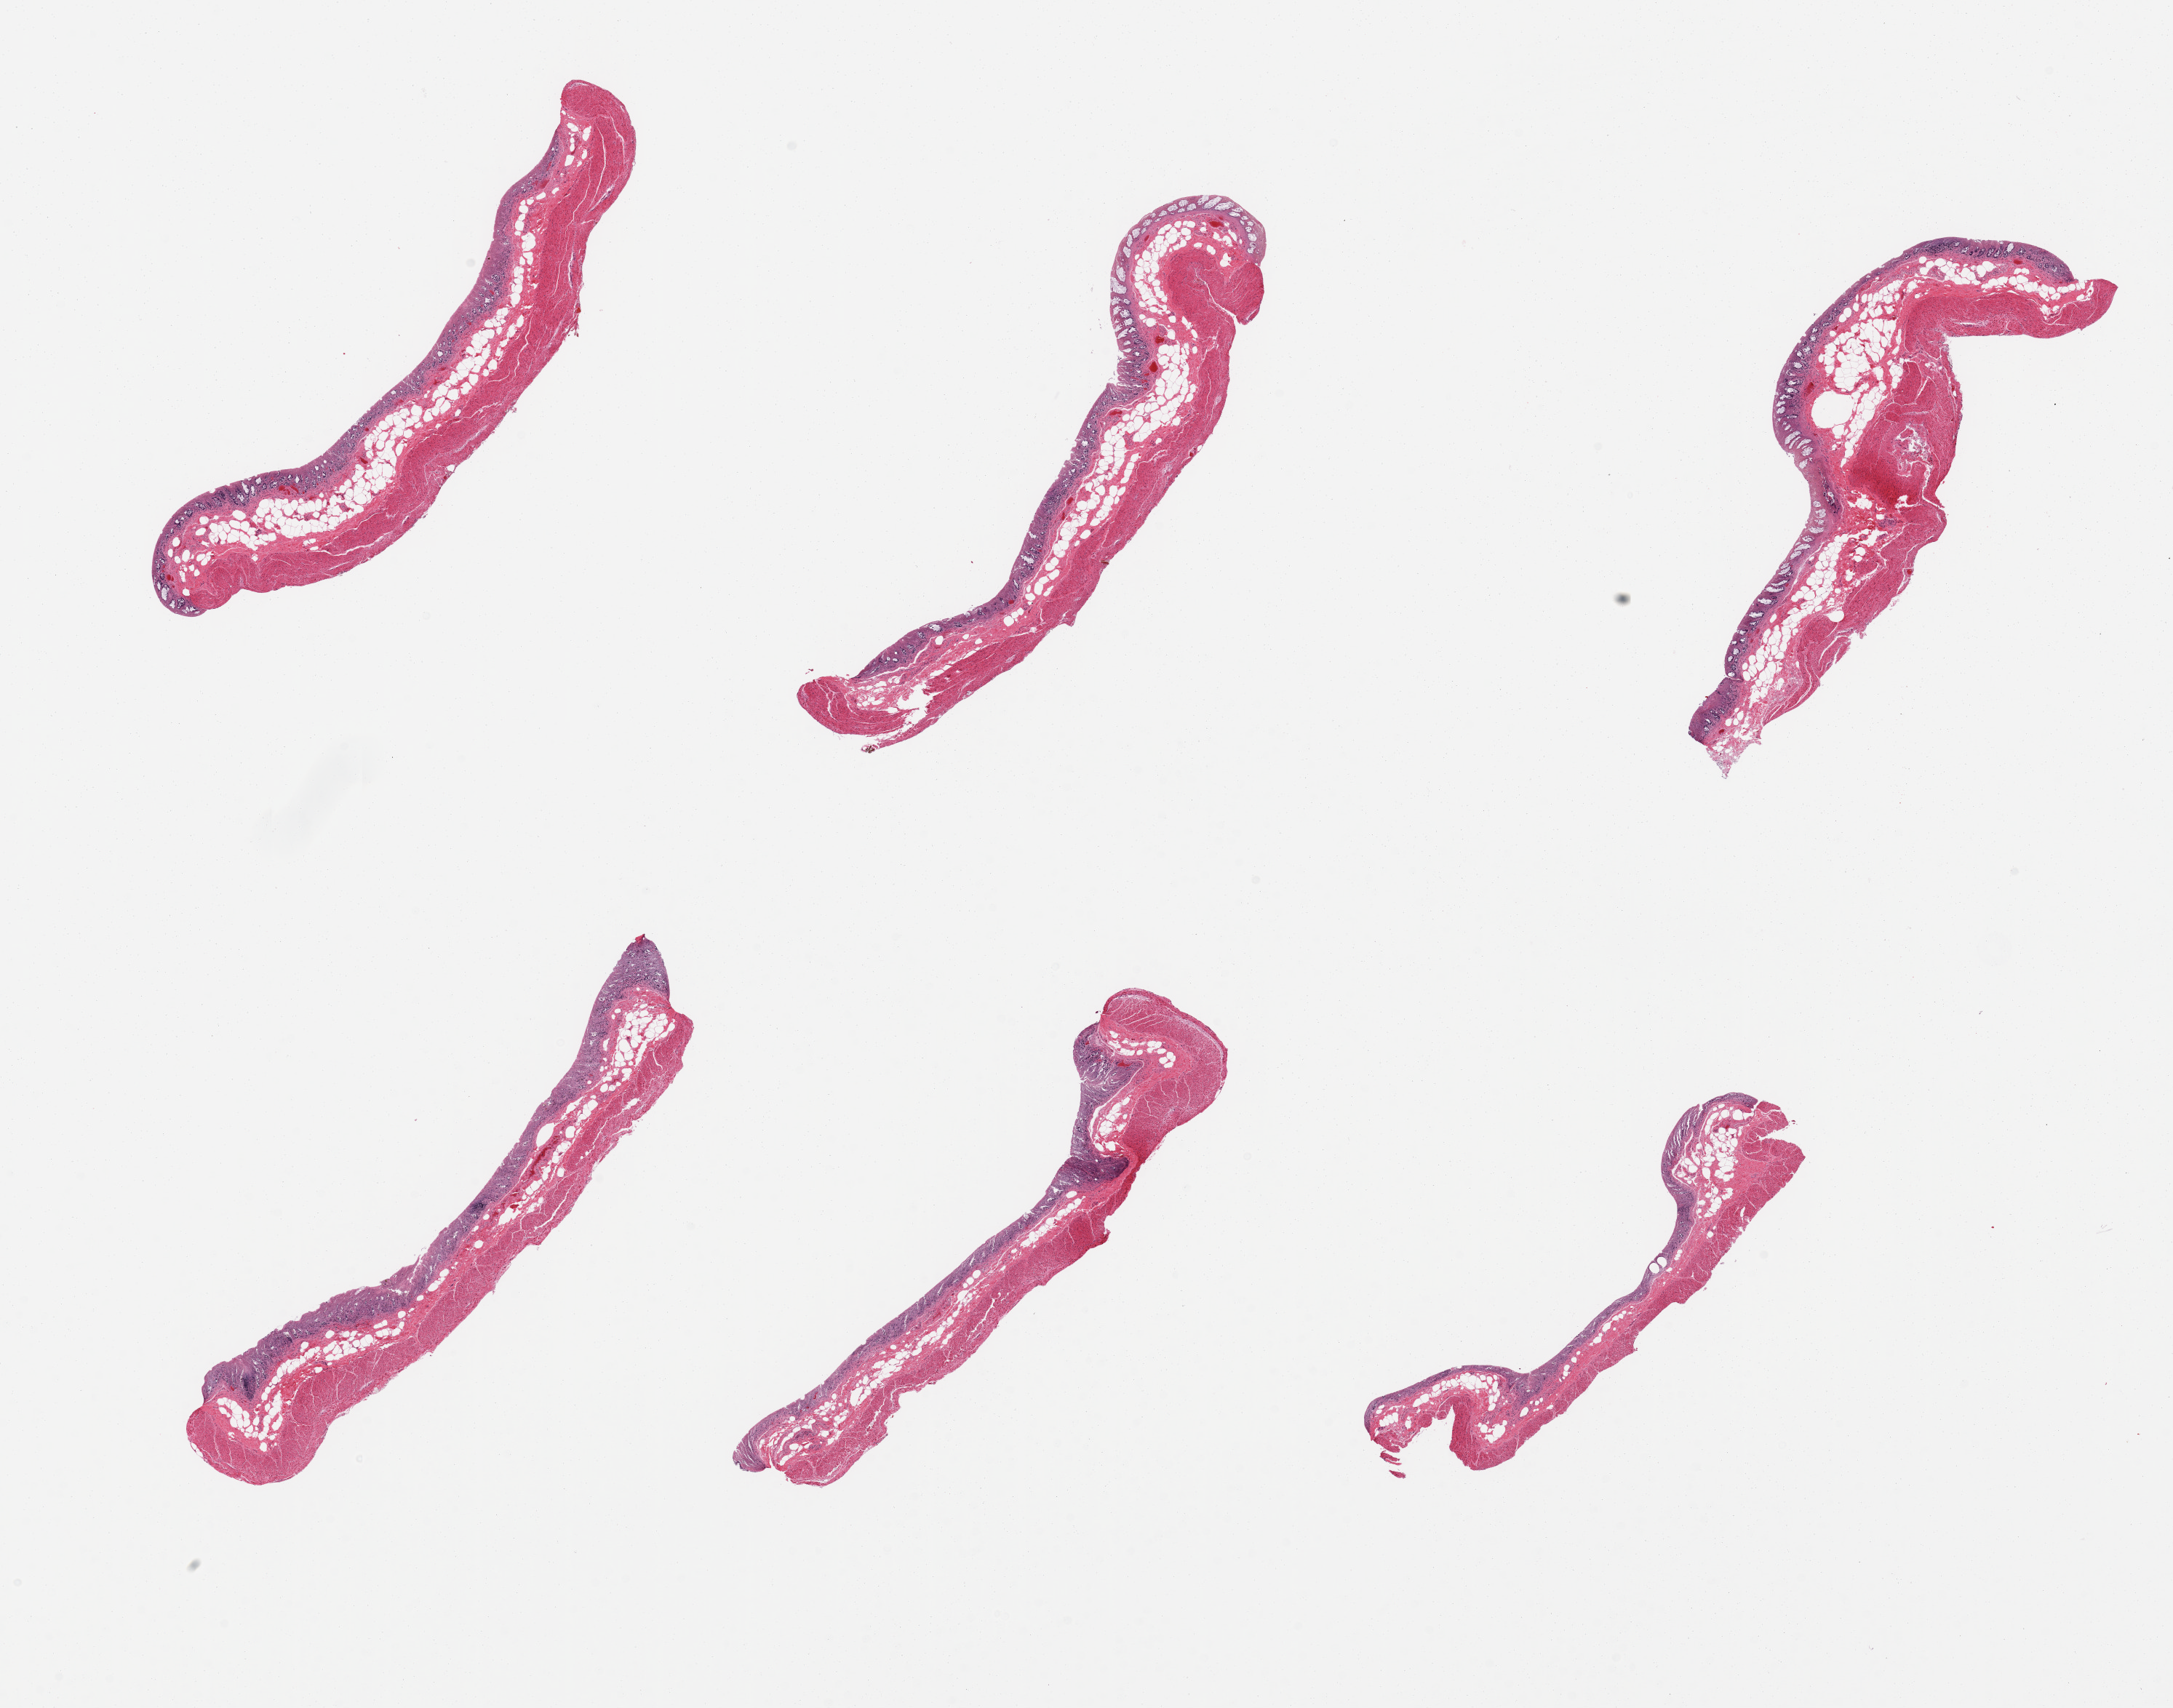
Whole-slide image, hematoxylin and eosin (H&E) stain, brightfield, whole scanned area (about 23.6 x 18.6 mm) shown as a low-resolution overview. PAXgene-fixed paraffin-embedded (PFPE) section. Target tissue: transverse colon. Donor tissue sample. Male donor.
• review note (as recorded): 6 pieces, severely autolyzed mucosa, muscularis